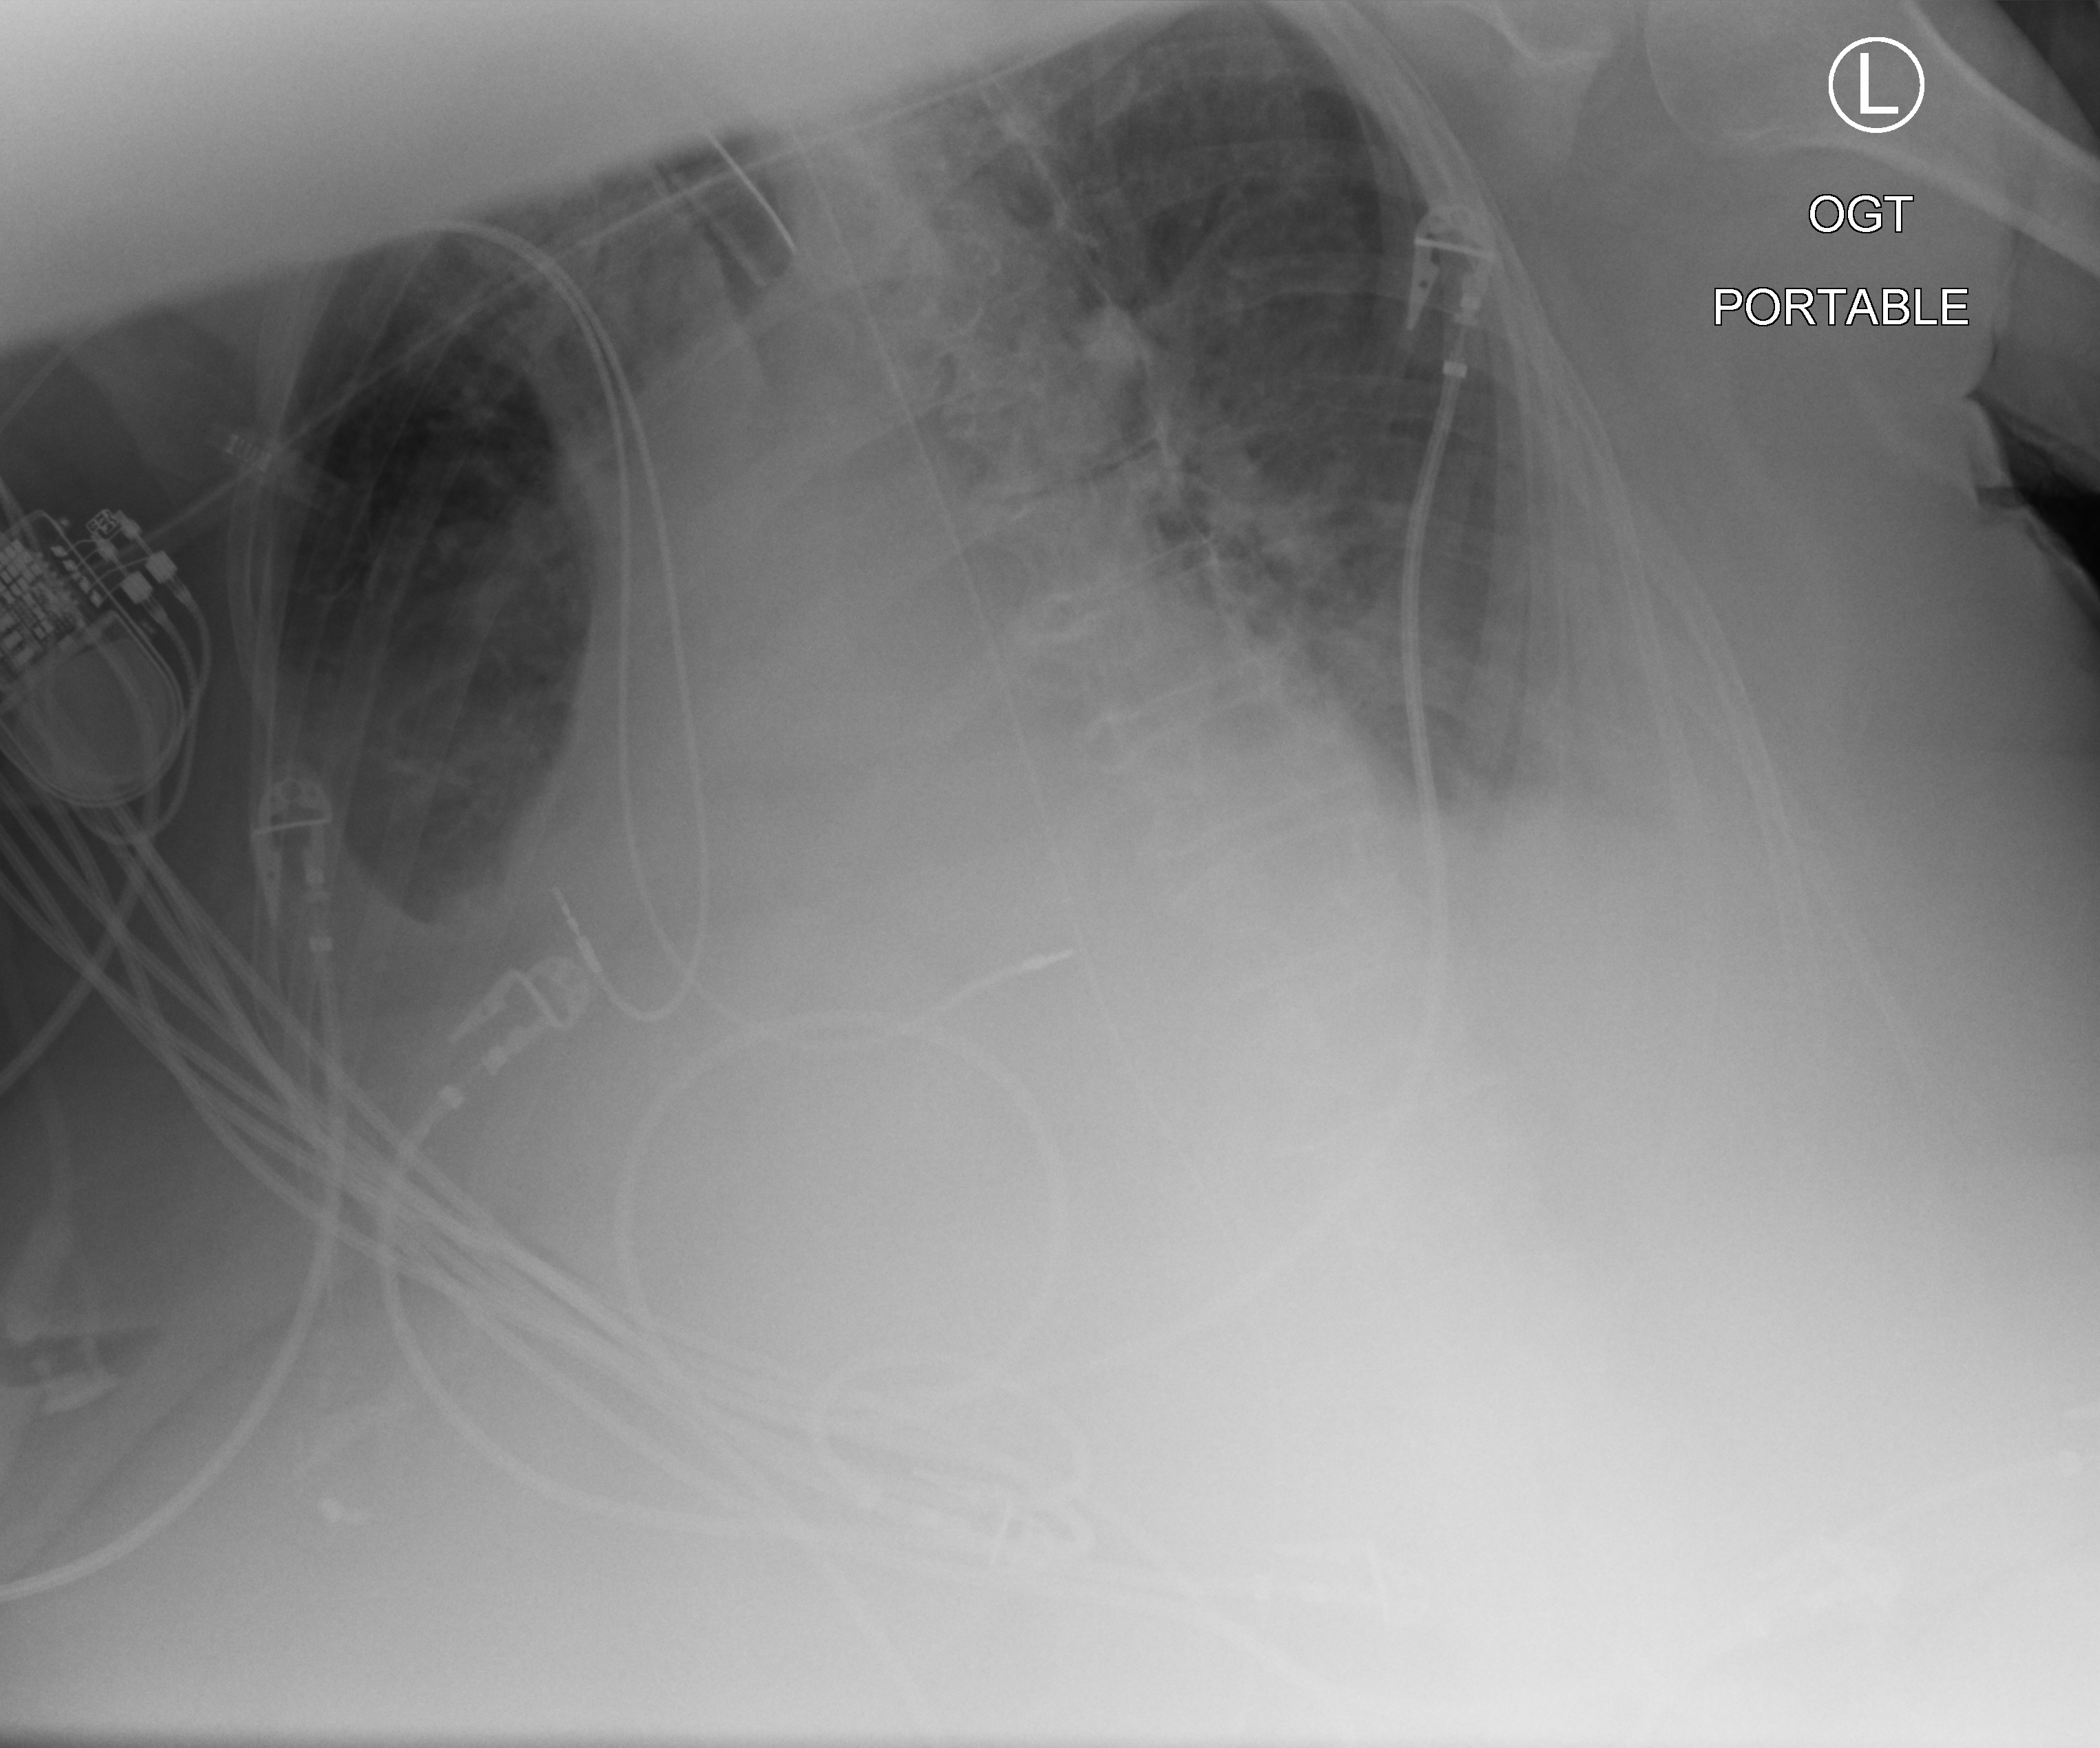
Bedside chest radiograph (computed radiography); anteroposterior (AP) projection. Female patient hospitalised with COVID-19, age 75–90 years.
From the hospital-stay record, not from the radiograph (when in the stay this image was taken is not recorded): admitted to intensive care during this hospital stay: yes.